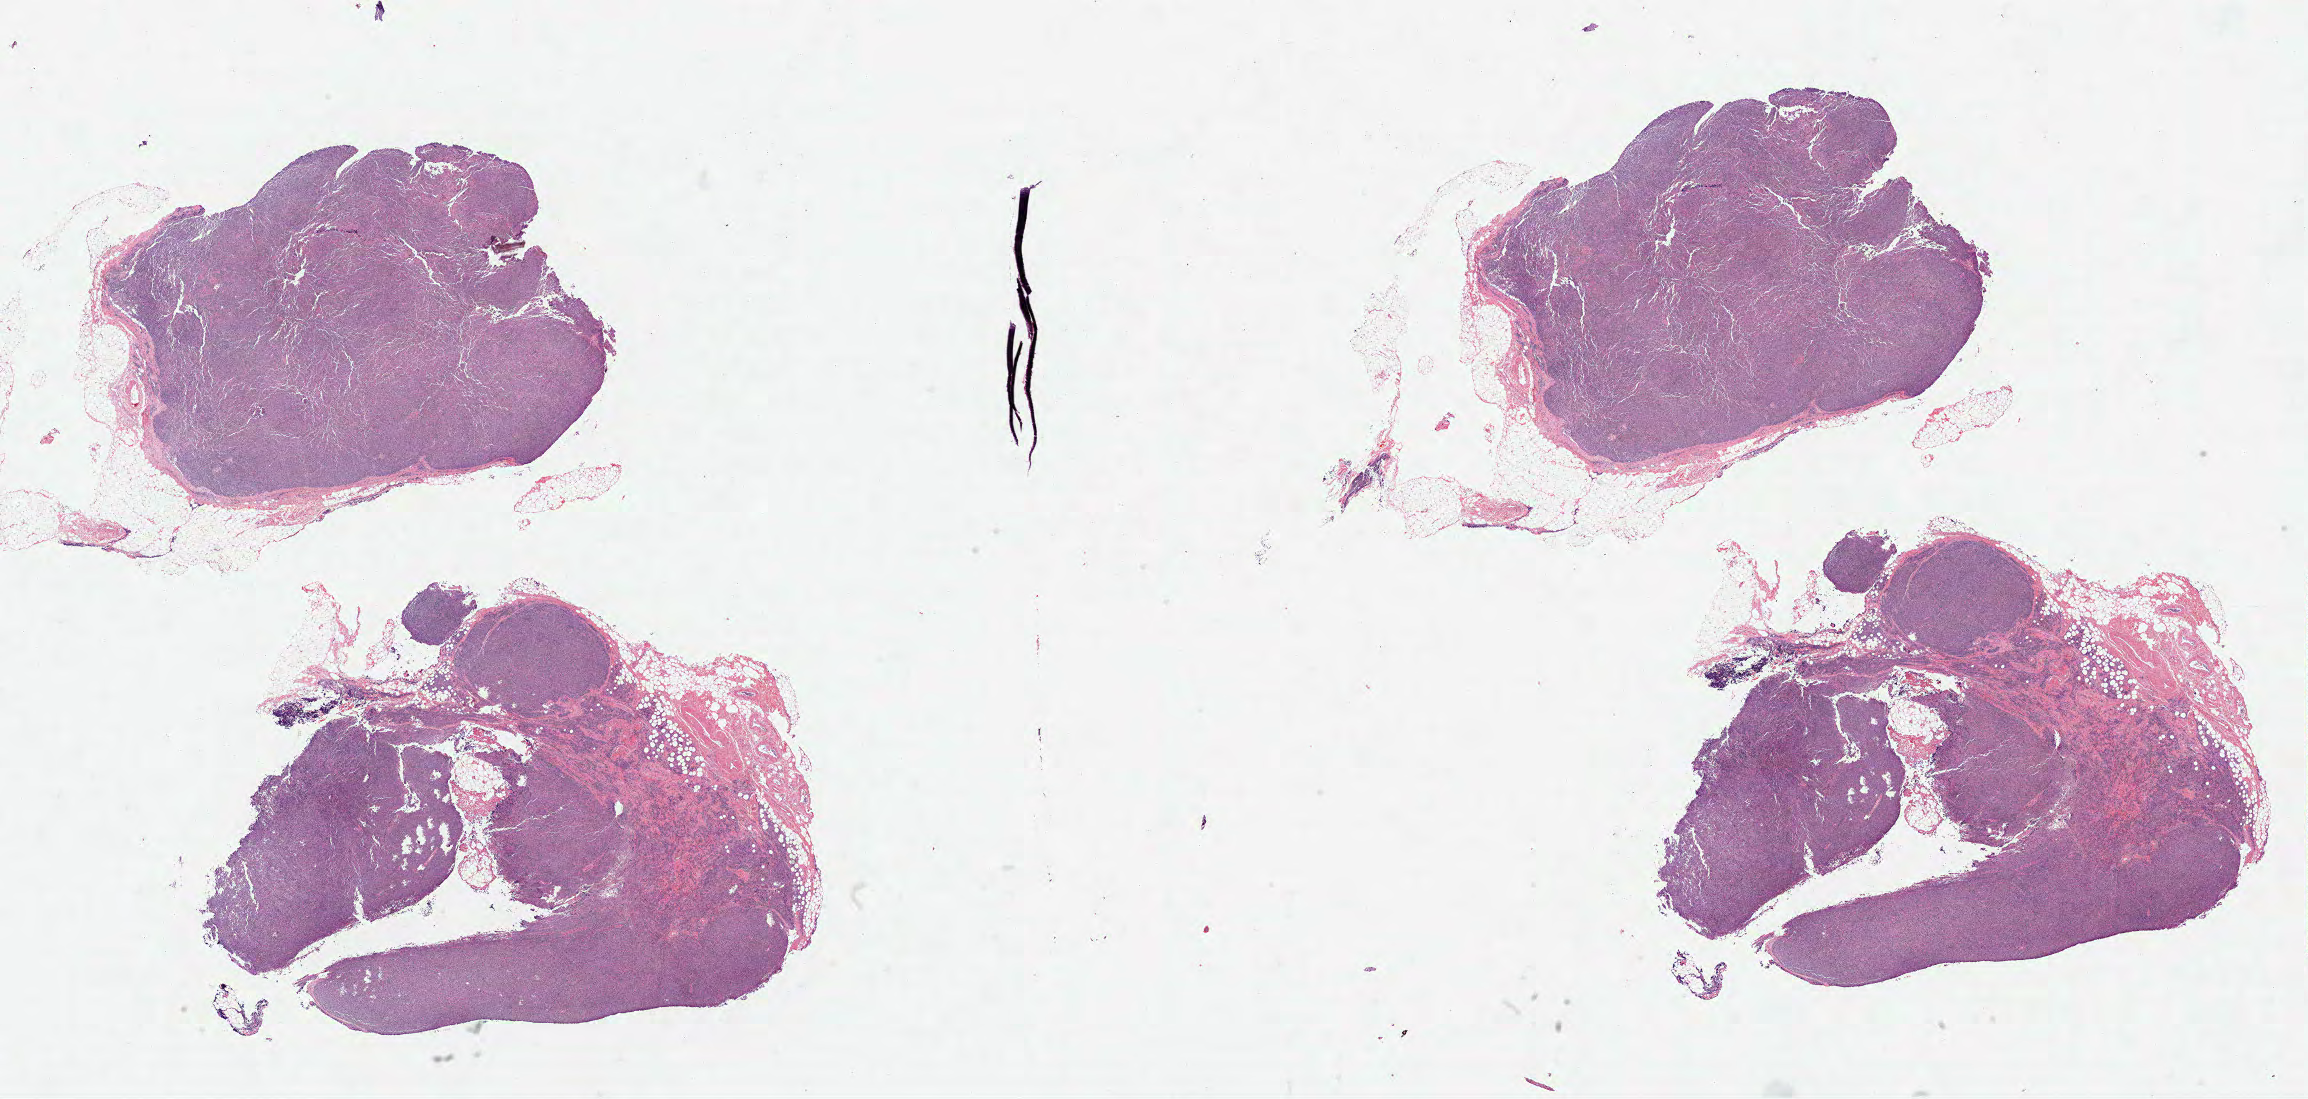
Whole-slide histology image, H&E-stained, a low-resolution overview of the entire scanned area, about 37.2 x 17.7 mm. Formalin-fixed paraffin-embedded (FFPE) diagnostic section. Primary tumour sample from the lymphoid tissue. Patient: female, age at initial diagnosis 43 years.
Pathologic diagnosis: Diffuse large B-cell lymphoma, NOS (intra-abdominal lymph nodes).